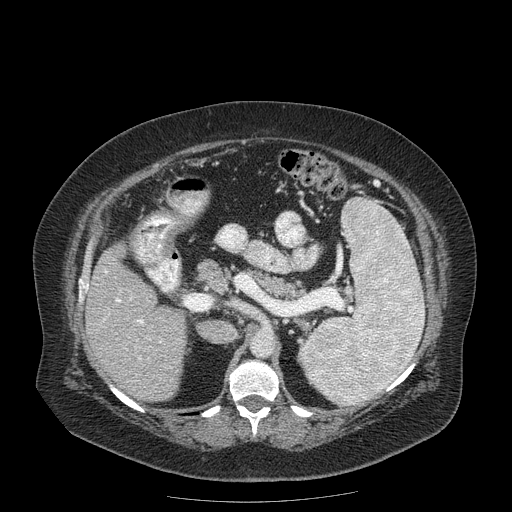
Contrast-enhanced abdominal CT (liver protocol), one axial slice. Reconstruction kernel STANDARD. 120 kVp. Soft-tissue window (W 400 / L 40 HU). 2.5 mm slice thickness. 512 × 512 image matrix. Case-level facts recorded for this patient, not image findings: diagnosis: hepatocellular carcinoma (patient treated with transarterial chemoembolisation; whether this scan precedes or follows treatment is not stated here); TNM stage (as recorded): Stage-IIIB; Child-Pugh class: A.
Annotated regions visible in this slice (semi-automatically segmented with operator editing):
- liver parenchyma outside the tumour (the mass and vessels are separate outlines, so this box may not span the whole liver): box from (x=86, y=244) to (x=186, y=402) px
- liver vessels: (x=103, y=270)–(x=144, y=359)